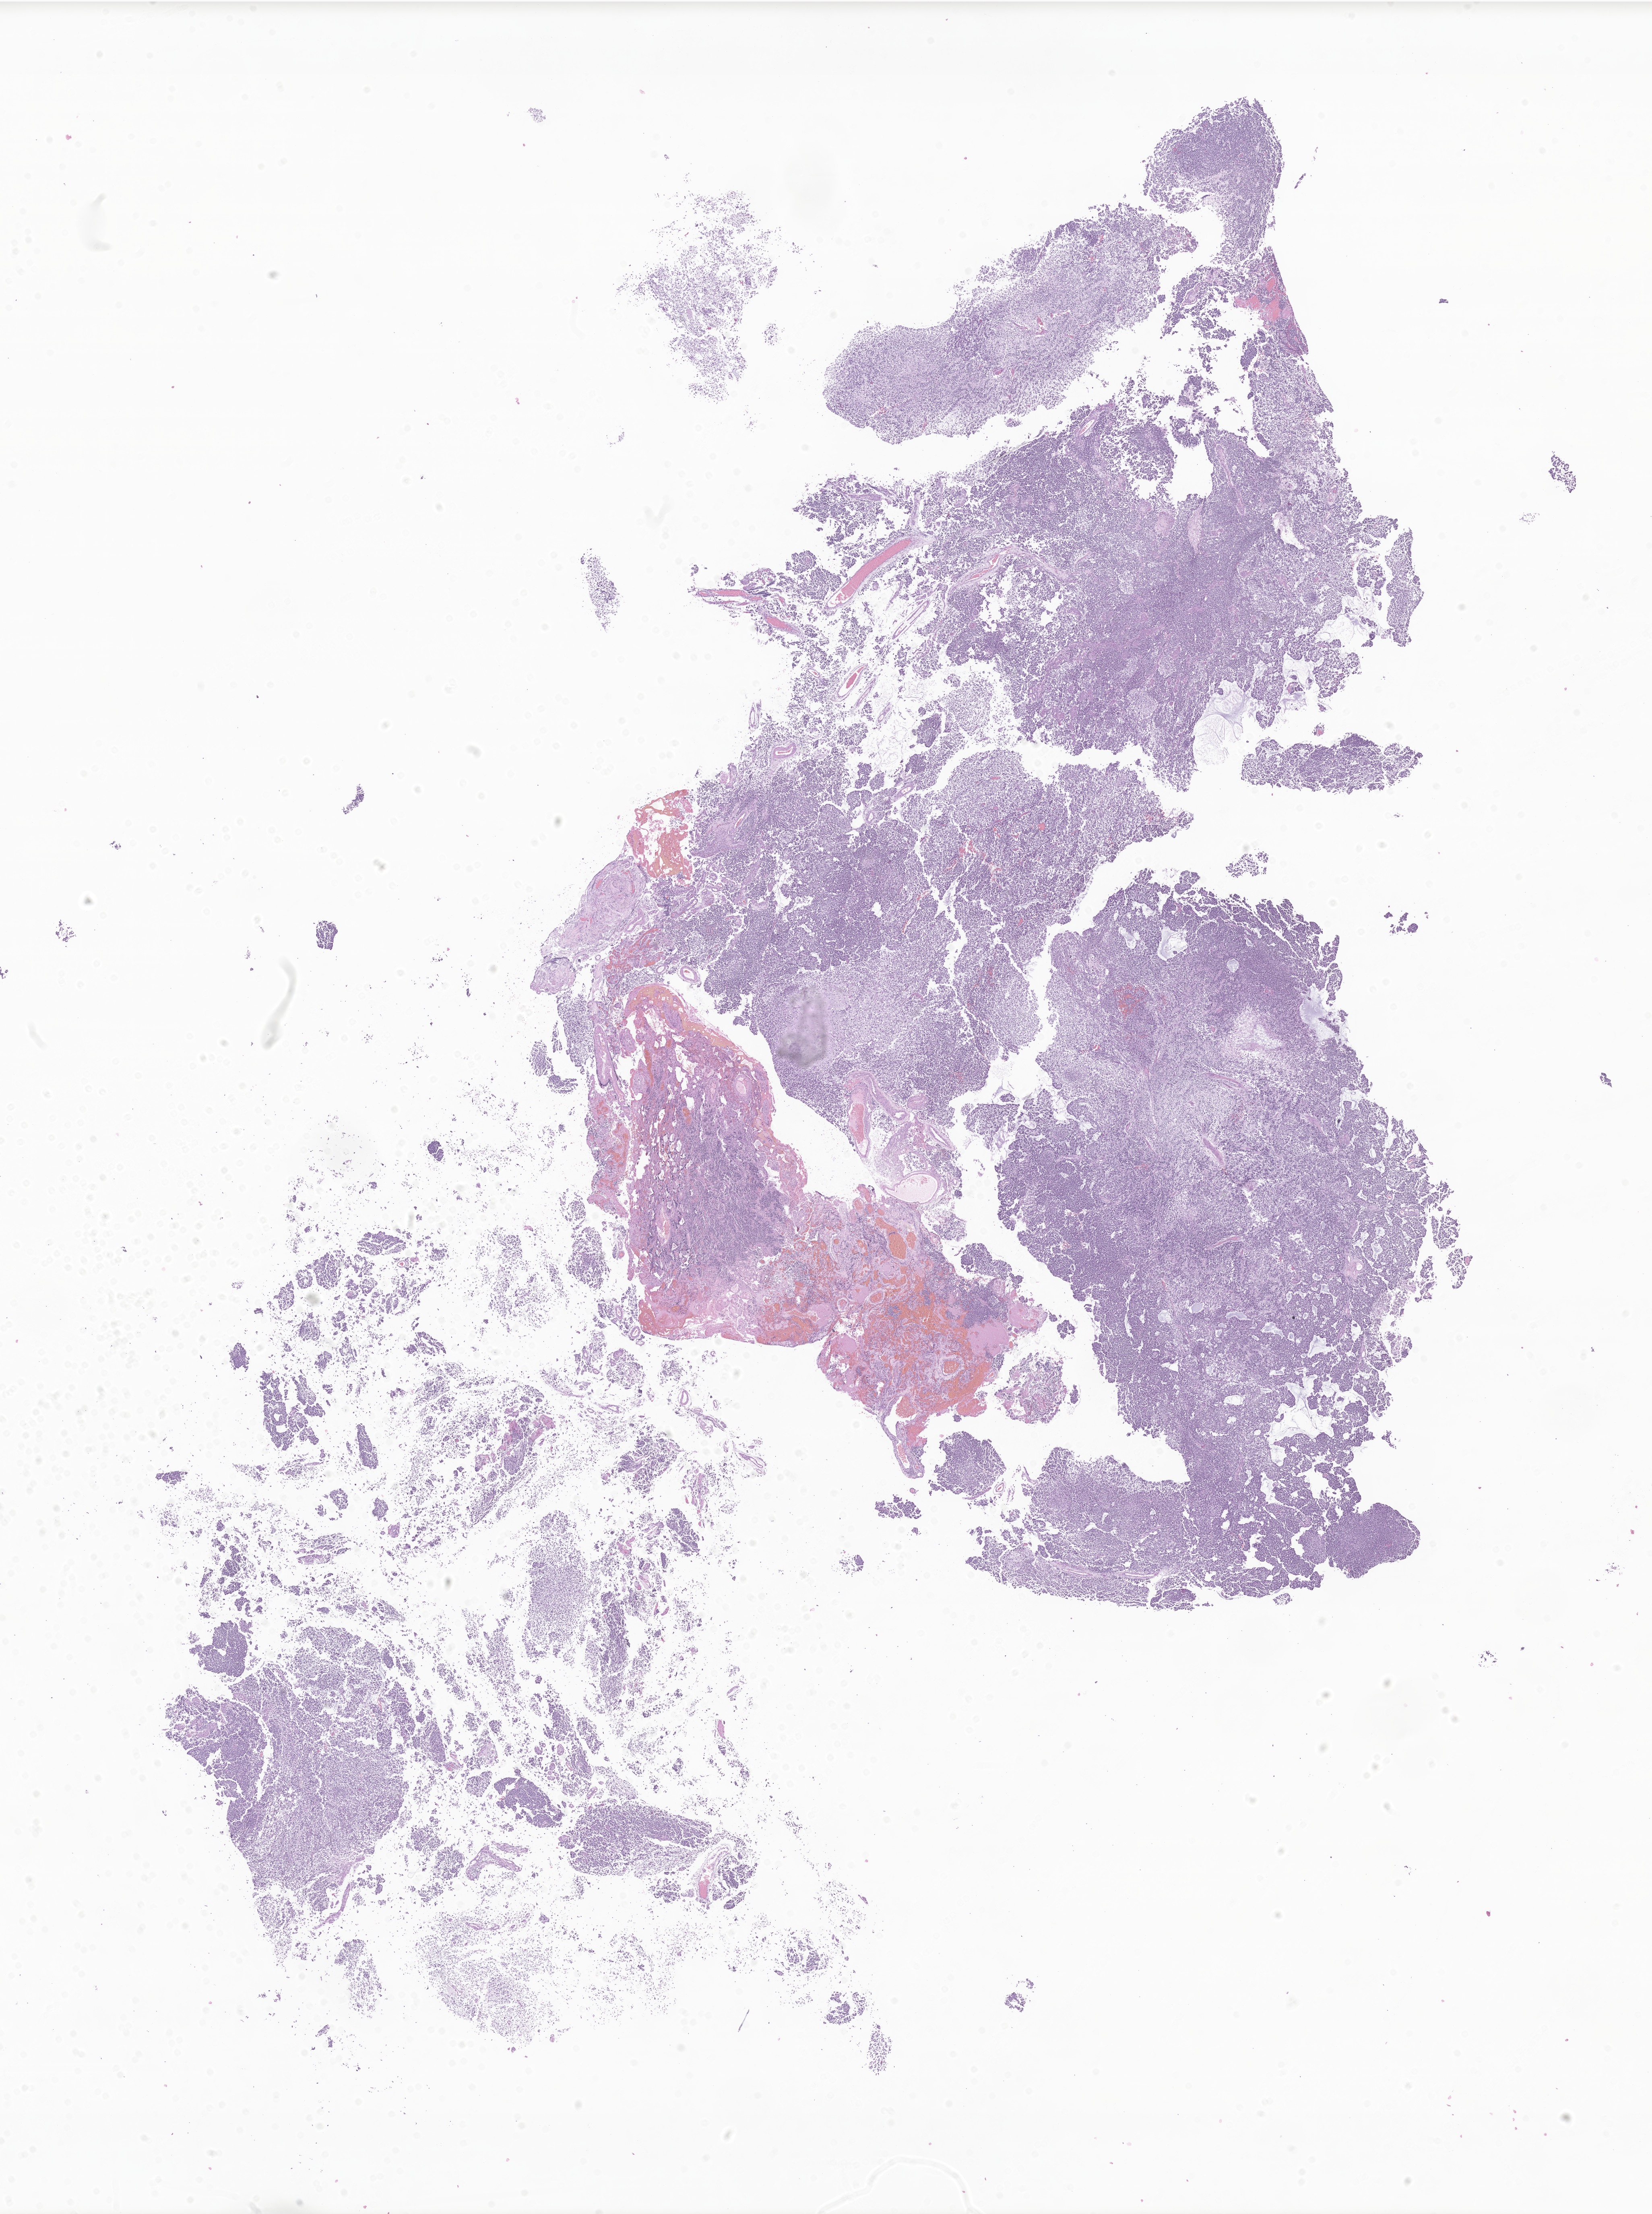
Digitized H&E-stained section of tumor tissue from the brain, whole scanned area (about 17.3 x 23.2 mm) shown as a low-resolution overview, formalin-fixed, paraffin-embedded (FFPE) tissue. Patient: male, age 51 months (4 years 3 months).
Recorded diagnosis: Medulloblastoma, NOS.